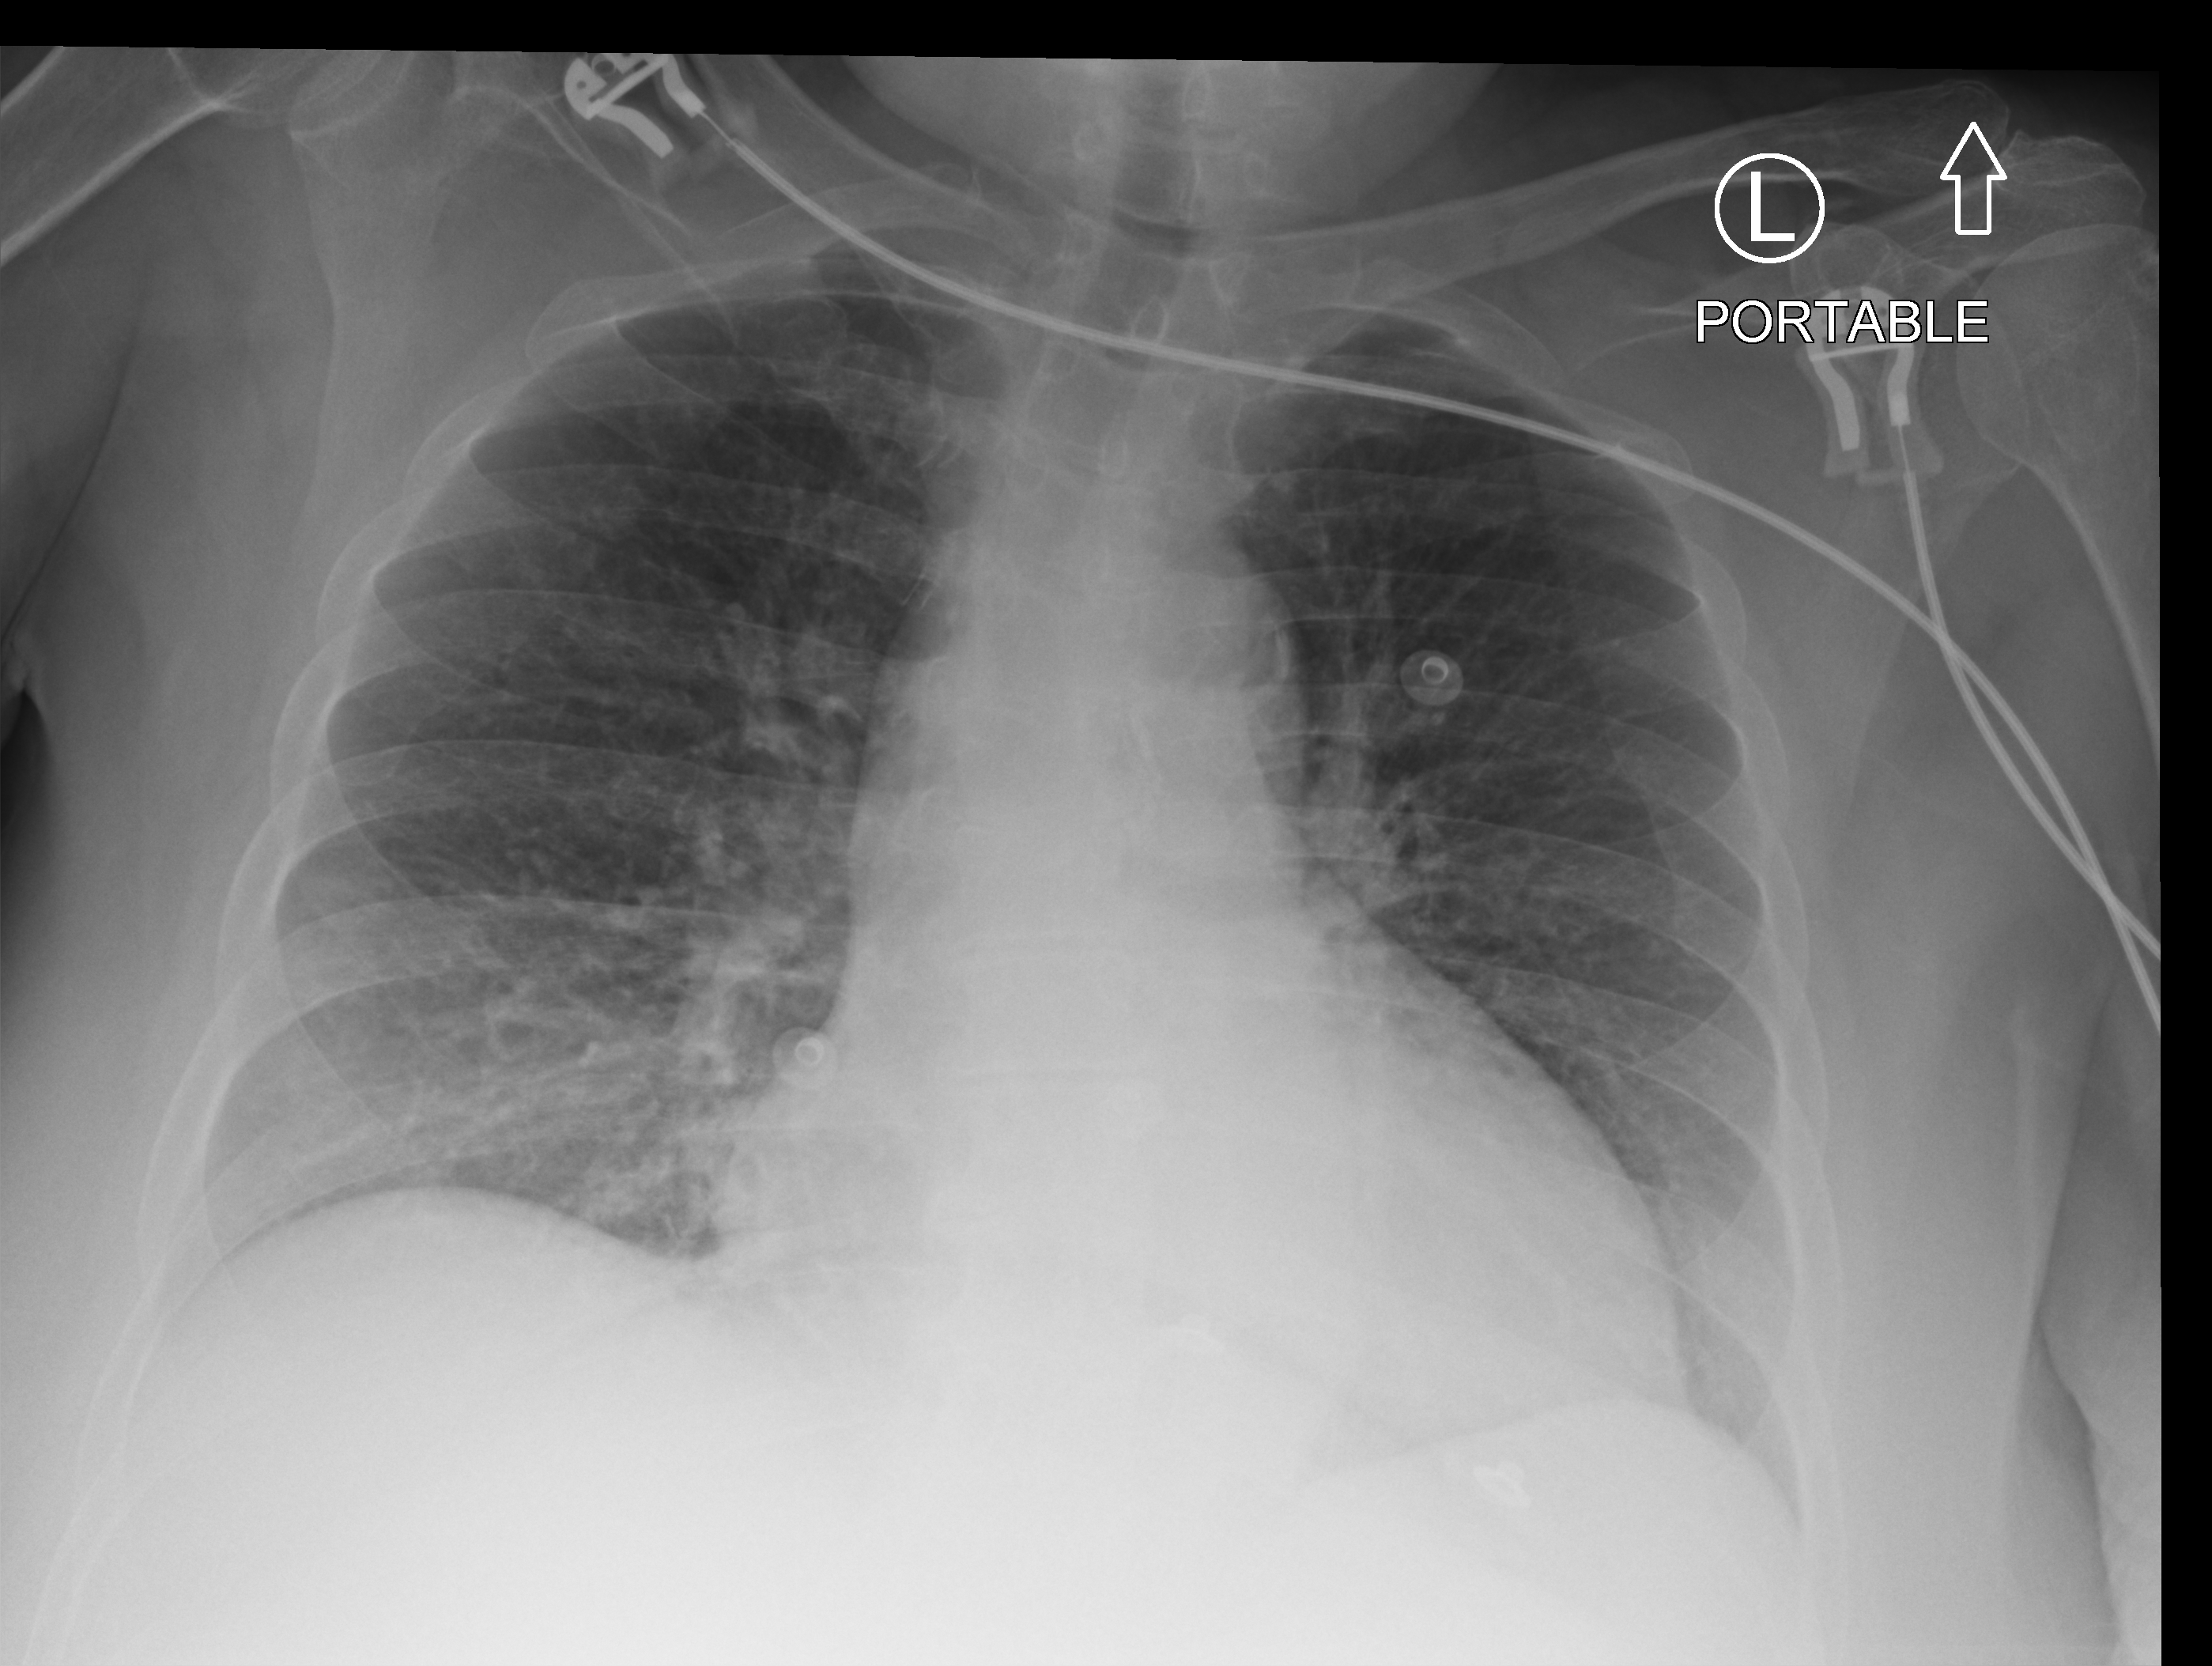
Portable chest radiograph; anteroposterior (AP) projection. Female patient hospitalised with COVID-19, age 60–74 years.
Admission-level facts for this patient (not findings on this image; timing relative to this image not recorded):
- other chronic lung disease (admission record): no
- mechanically ventilated during this hospital stay: no